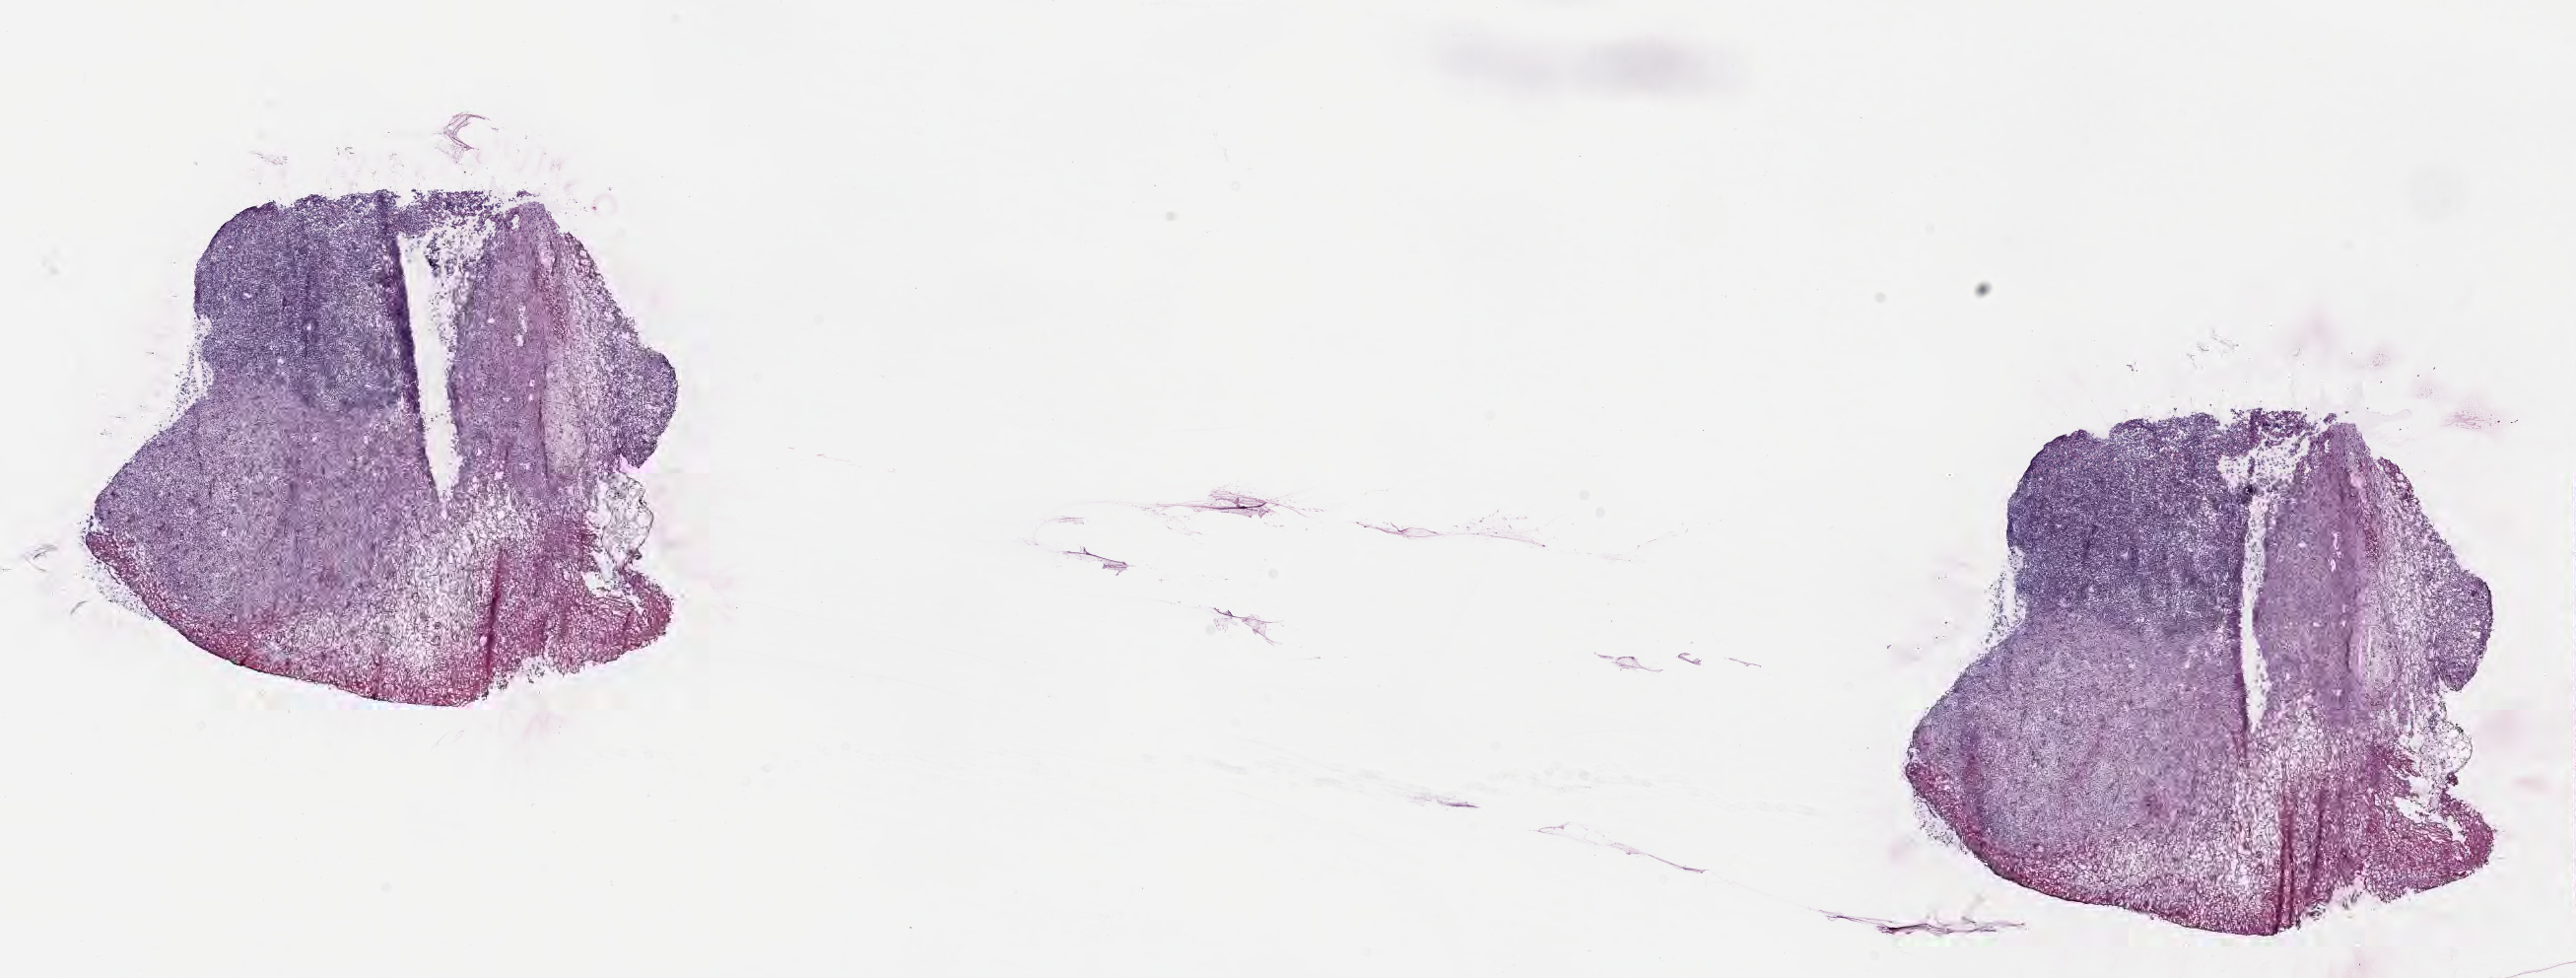
H&E whole-slide image — low-resolution overview of the scanned area, about 21.1 x 8.0 mm, cryosection, primary tumor, site: cranium. Male, age 2 years at initial diagnosis. Composition of this section per pathologist review: tumor cells 25%, tumor nuclei 80%, stromal cells 65%, necrosis 10%, normal cells 0%. Infiltration values recorded for this section: lymphocyte infiltration 30%, monocyte infiltration 35%, neutrophil infiltration 15%.
Ann Arbor stage (patient): Stage I. Diagnosis: Burkitt lymphoma, NOS.